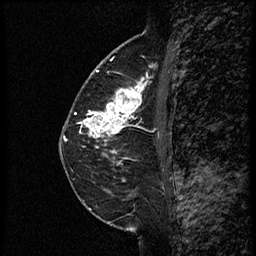
Breast MRI (dynamic contrast-enhanced), one sagittal slice; dynamic contrast-enhanced study with each time point stored as its own series, time point 2 of 3 at this slice position (early post-contrast, ordered by acquisition time); 1.5 T; TE 4.2 ms, TR 18.9 ms; 2 mm slice thickness; 256 × 256 image matrix, field of view 200 × 200 mm. Female patient. Case-level facts recorded for this patient, not image findings: setting: breast cancer imaged before/during neoadjuvant chemotherapy; receptor status: HER2-positive.
Structures marked on this image (semi-automatic segmentation, software-assisted and operator-edited):
- analysis volume of interest (the breast-tissue region the enhancement analysis was run in; not a lesion): bounding box (x1, y1, x2, y2) in pixels: (81, 66, 161, 147)
- tumour enhancement mask (voxels above the 100 % enhancement threshold inside the analysis volume of interest): (85, 77, 151, 146)